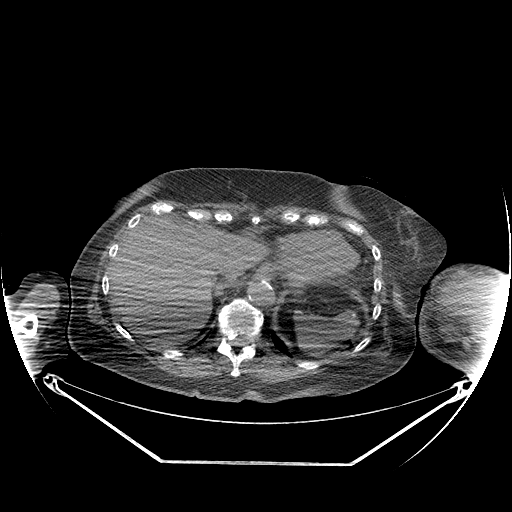
CT of an extremity soft-tissue mass (from a PET/CT study), one axial slice. Slice 139 of 267 in the series (ordered by position). Reconstruction kernel STANDARD. Soft-tissue window (W 400 / L 40 HU). 3.75 mm slice thickness. 512 × 512 image matrix, field of view 500 × 500 mm. Female patient. Case-level facts recorded for this patient, not image findings: histological type: pleiomorphic leiomyosarcoma; grade: high; site of the primary tumour: left biceps.
Structures marked on this image (expert contour drawn on MRI and transferred to this co-registered scan by the dataset authors):
- gross tumour volume including surrounding oedema: box from (x=475, y=294) to (x=496, y=316) px